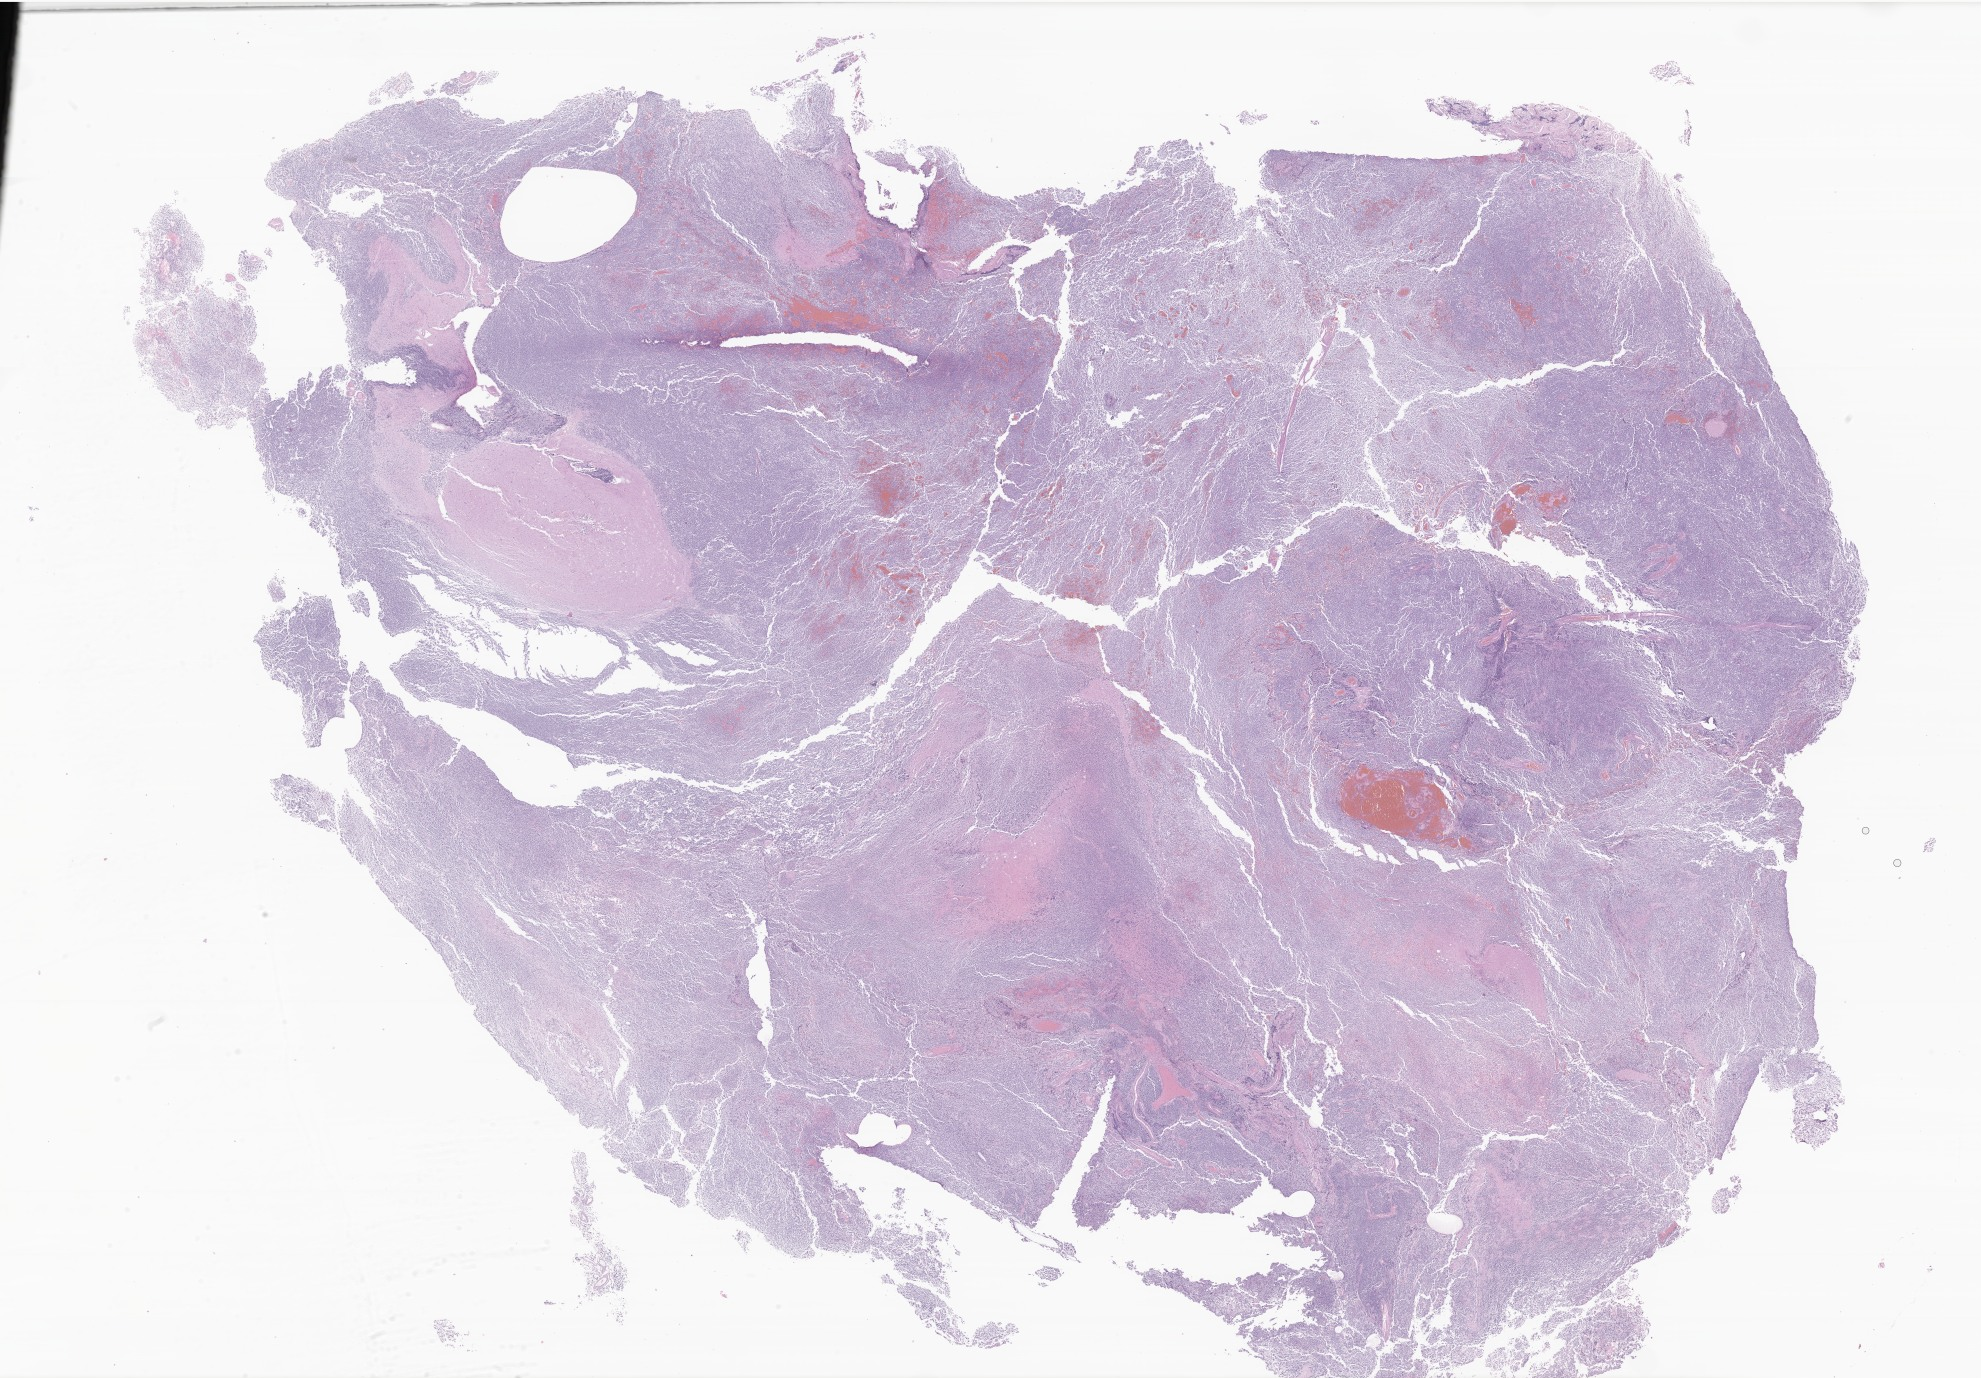
Whole-slide image, hematoxylin and eosin (H&E) stain of tumor tissue from the brain, whole scanned area (about 33.4 x 23.2 mm) shown as a low-resolution overview, formalin-fixed, paraffin-embedded (FFPE) tissue. Patient male; age 138 months (11 years 6 months).
Diagnosis (ICD-O-3 morphology term): Medulloblastoma, NOS.